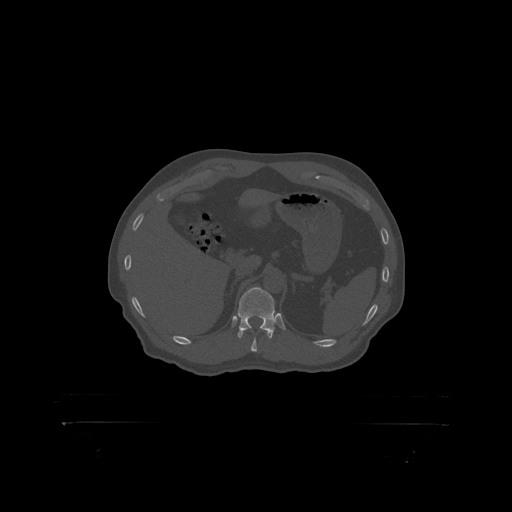
CT including the spine, one axial slice; slice 362 of 399 in the series (ordered by position); reconstruction kernel STANDARD; bone window (W 1800 / L 400 HU); 1.25 mm slice thickness; 512 × 512 image matrix, field of view 650 × 650 mm. Male patient, age 46 years. Case-level facts recorded for this patient, not image findings: primary cancer: skin.
Annotated regions visible in this slice (semi-automatic segmentation, software-assisted and operator-edited):
- T12 vertebra: bounding box <238,288,280,319> (left, top, right, bottom; pixels)